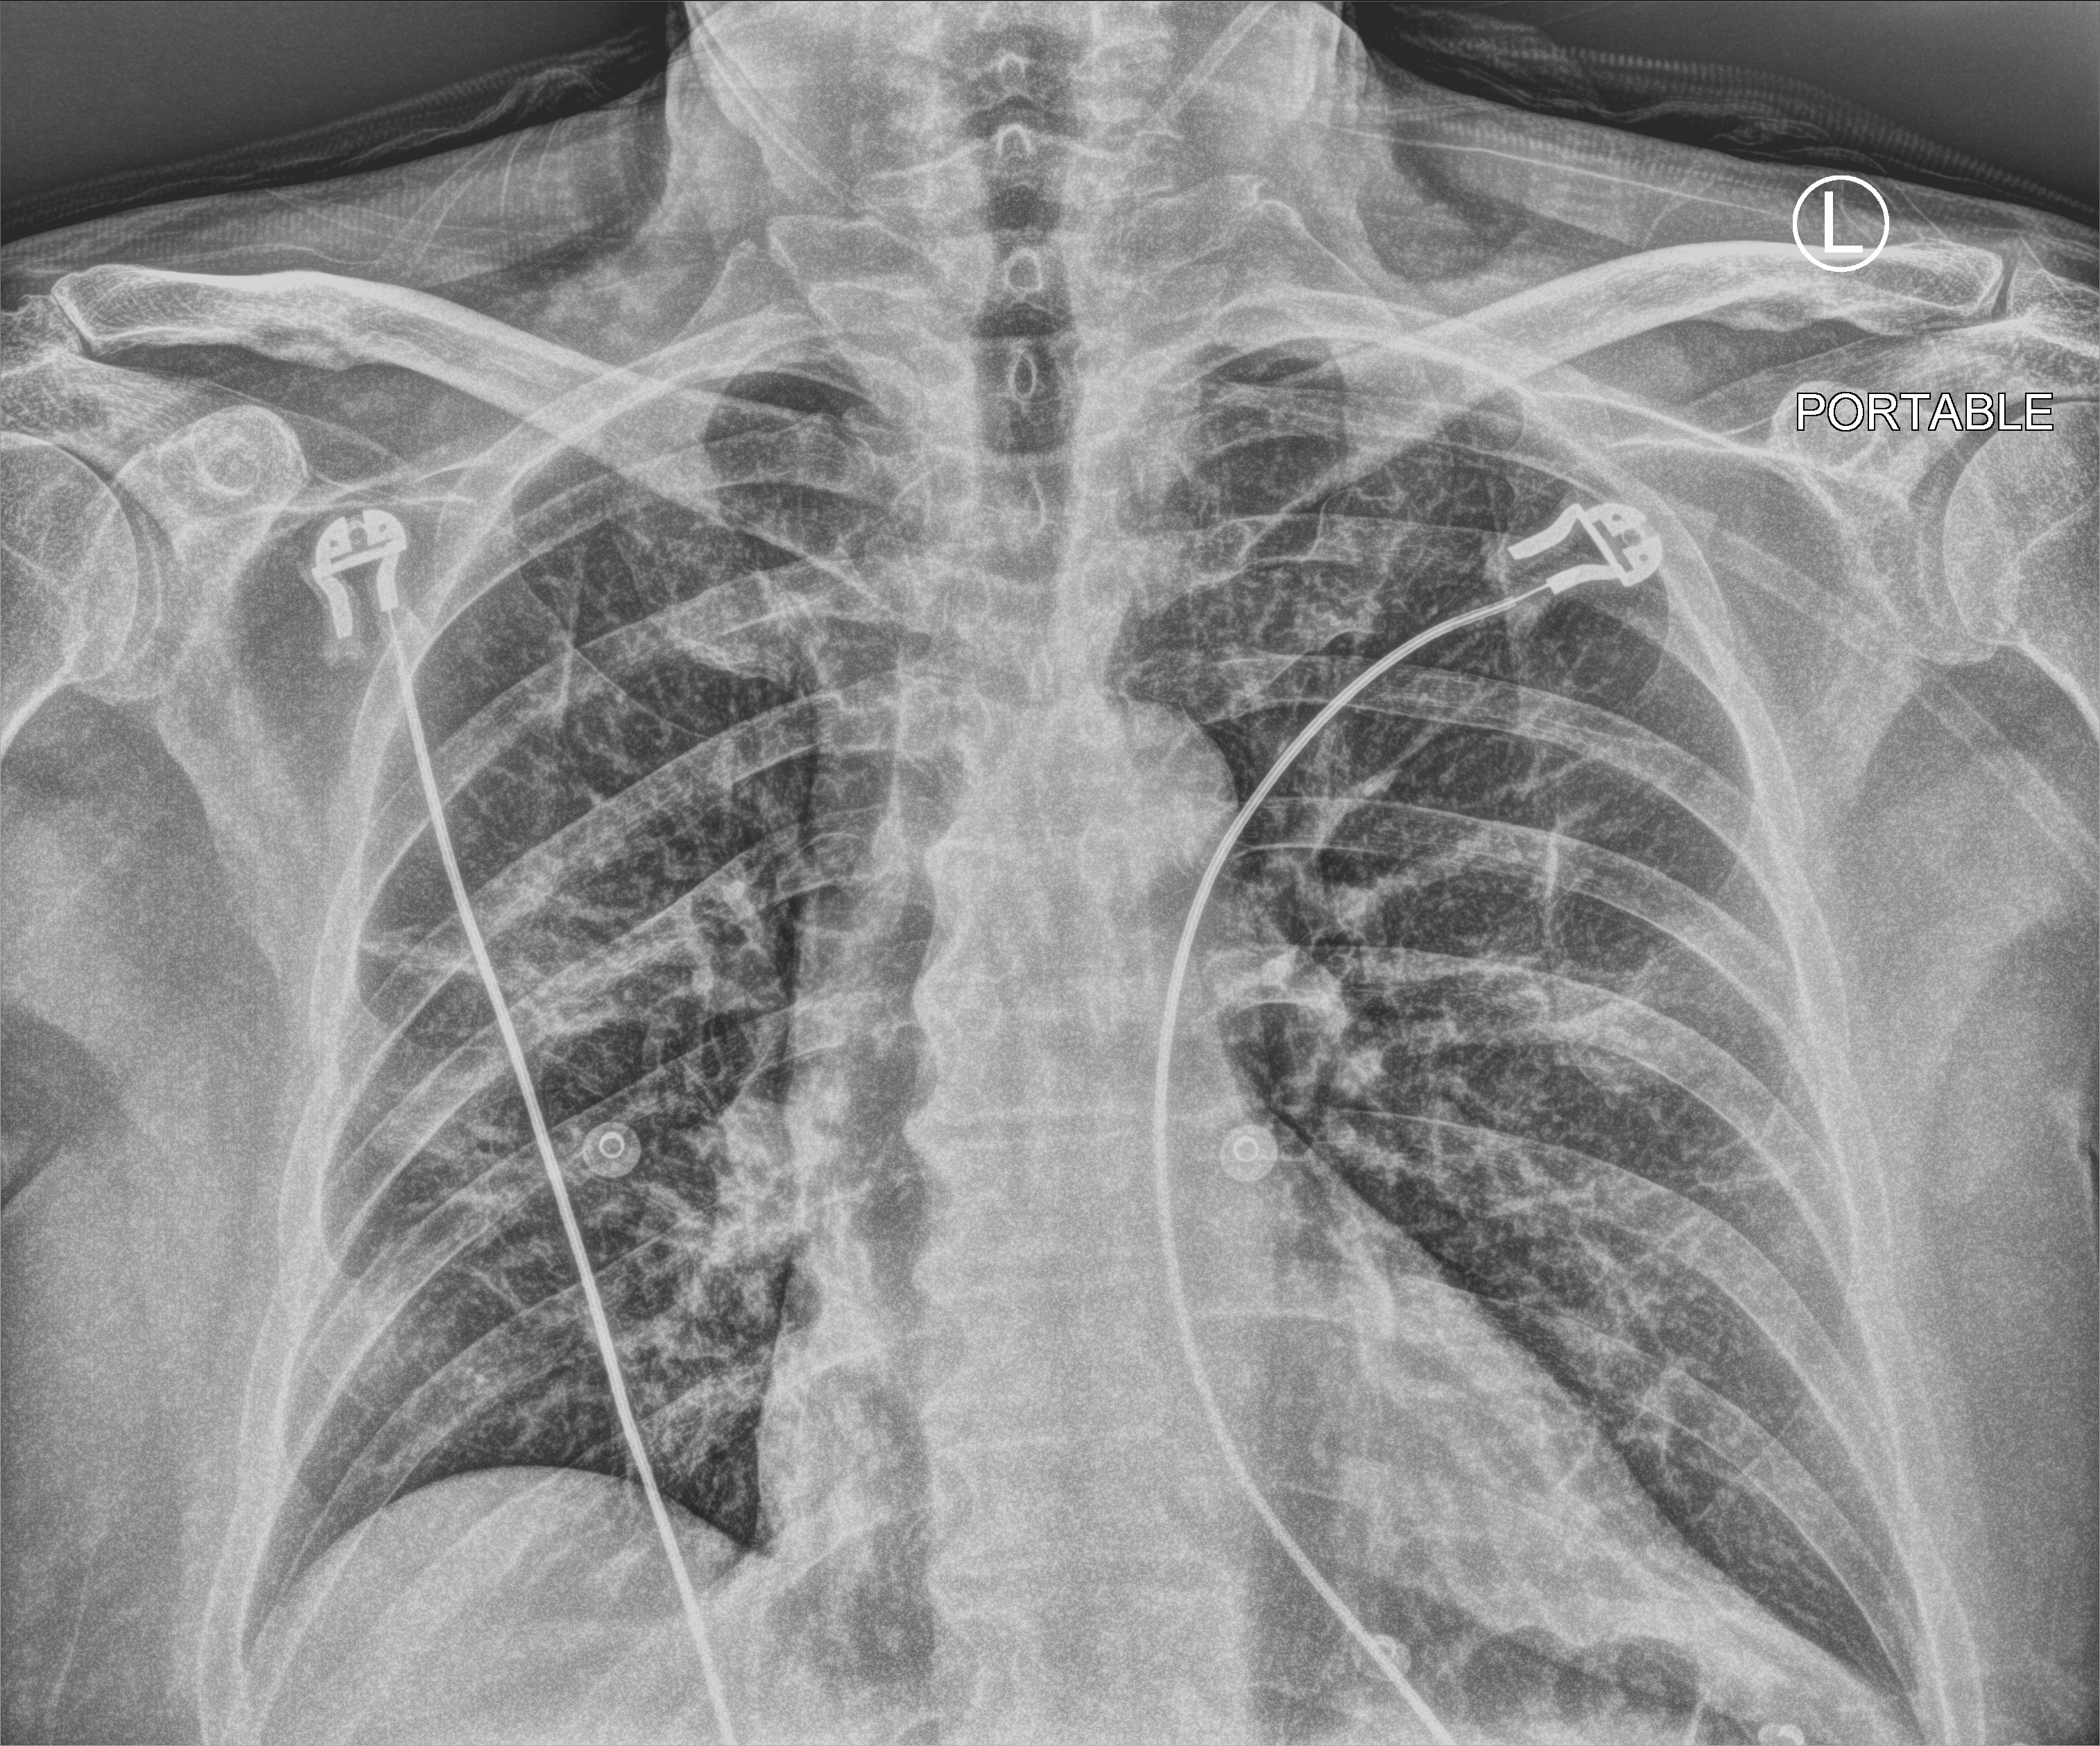
Bedside chest radiograph (computed radiography); anteroposterior (AP) projection. Patient hospitalised with COVID-19; male, aged 60–74 years.
From the hospital-stay record, not from the radiograph (when in the stay this image was taken is not recorded):
- mechanically ventilated during this hospital stay: no